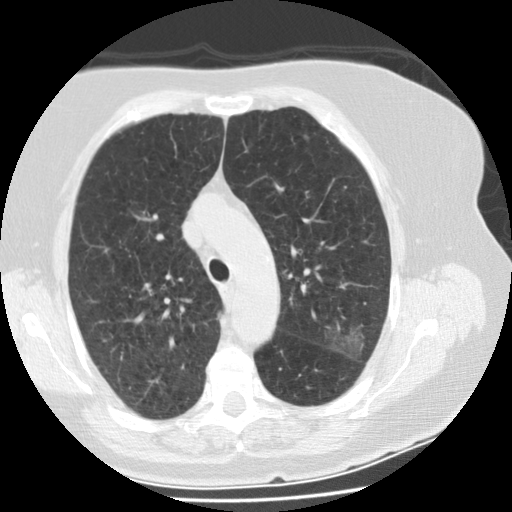
Low-dose screening chest CT, one axial slice; slice 112 of 151 in the series (ordered by position); 120 kVp; one of 2 acquisitions stored at this slice position; lung window (W 1500 / L -600 HU); 2.5 mm slice thickness; 512 × 512 image matrix.
Annotated regions visible in this slice (expert manual segmentation):
- lesion 1 (tumor, upper lobe of left lung): bounding box <327,323,363,356> (left, top, right, bottom; pixels)